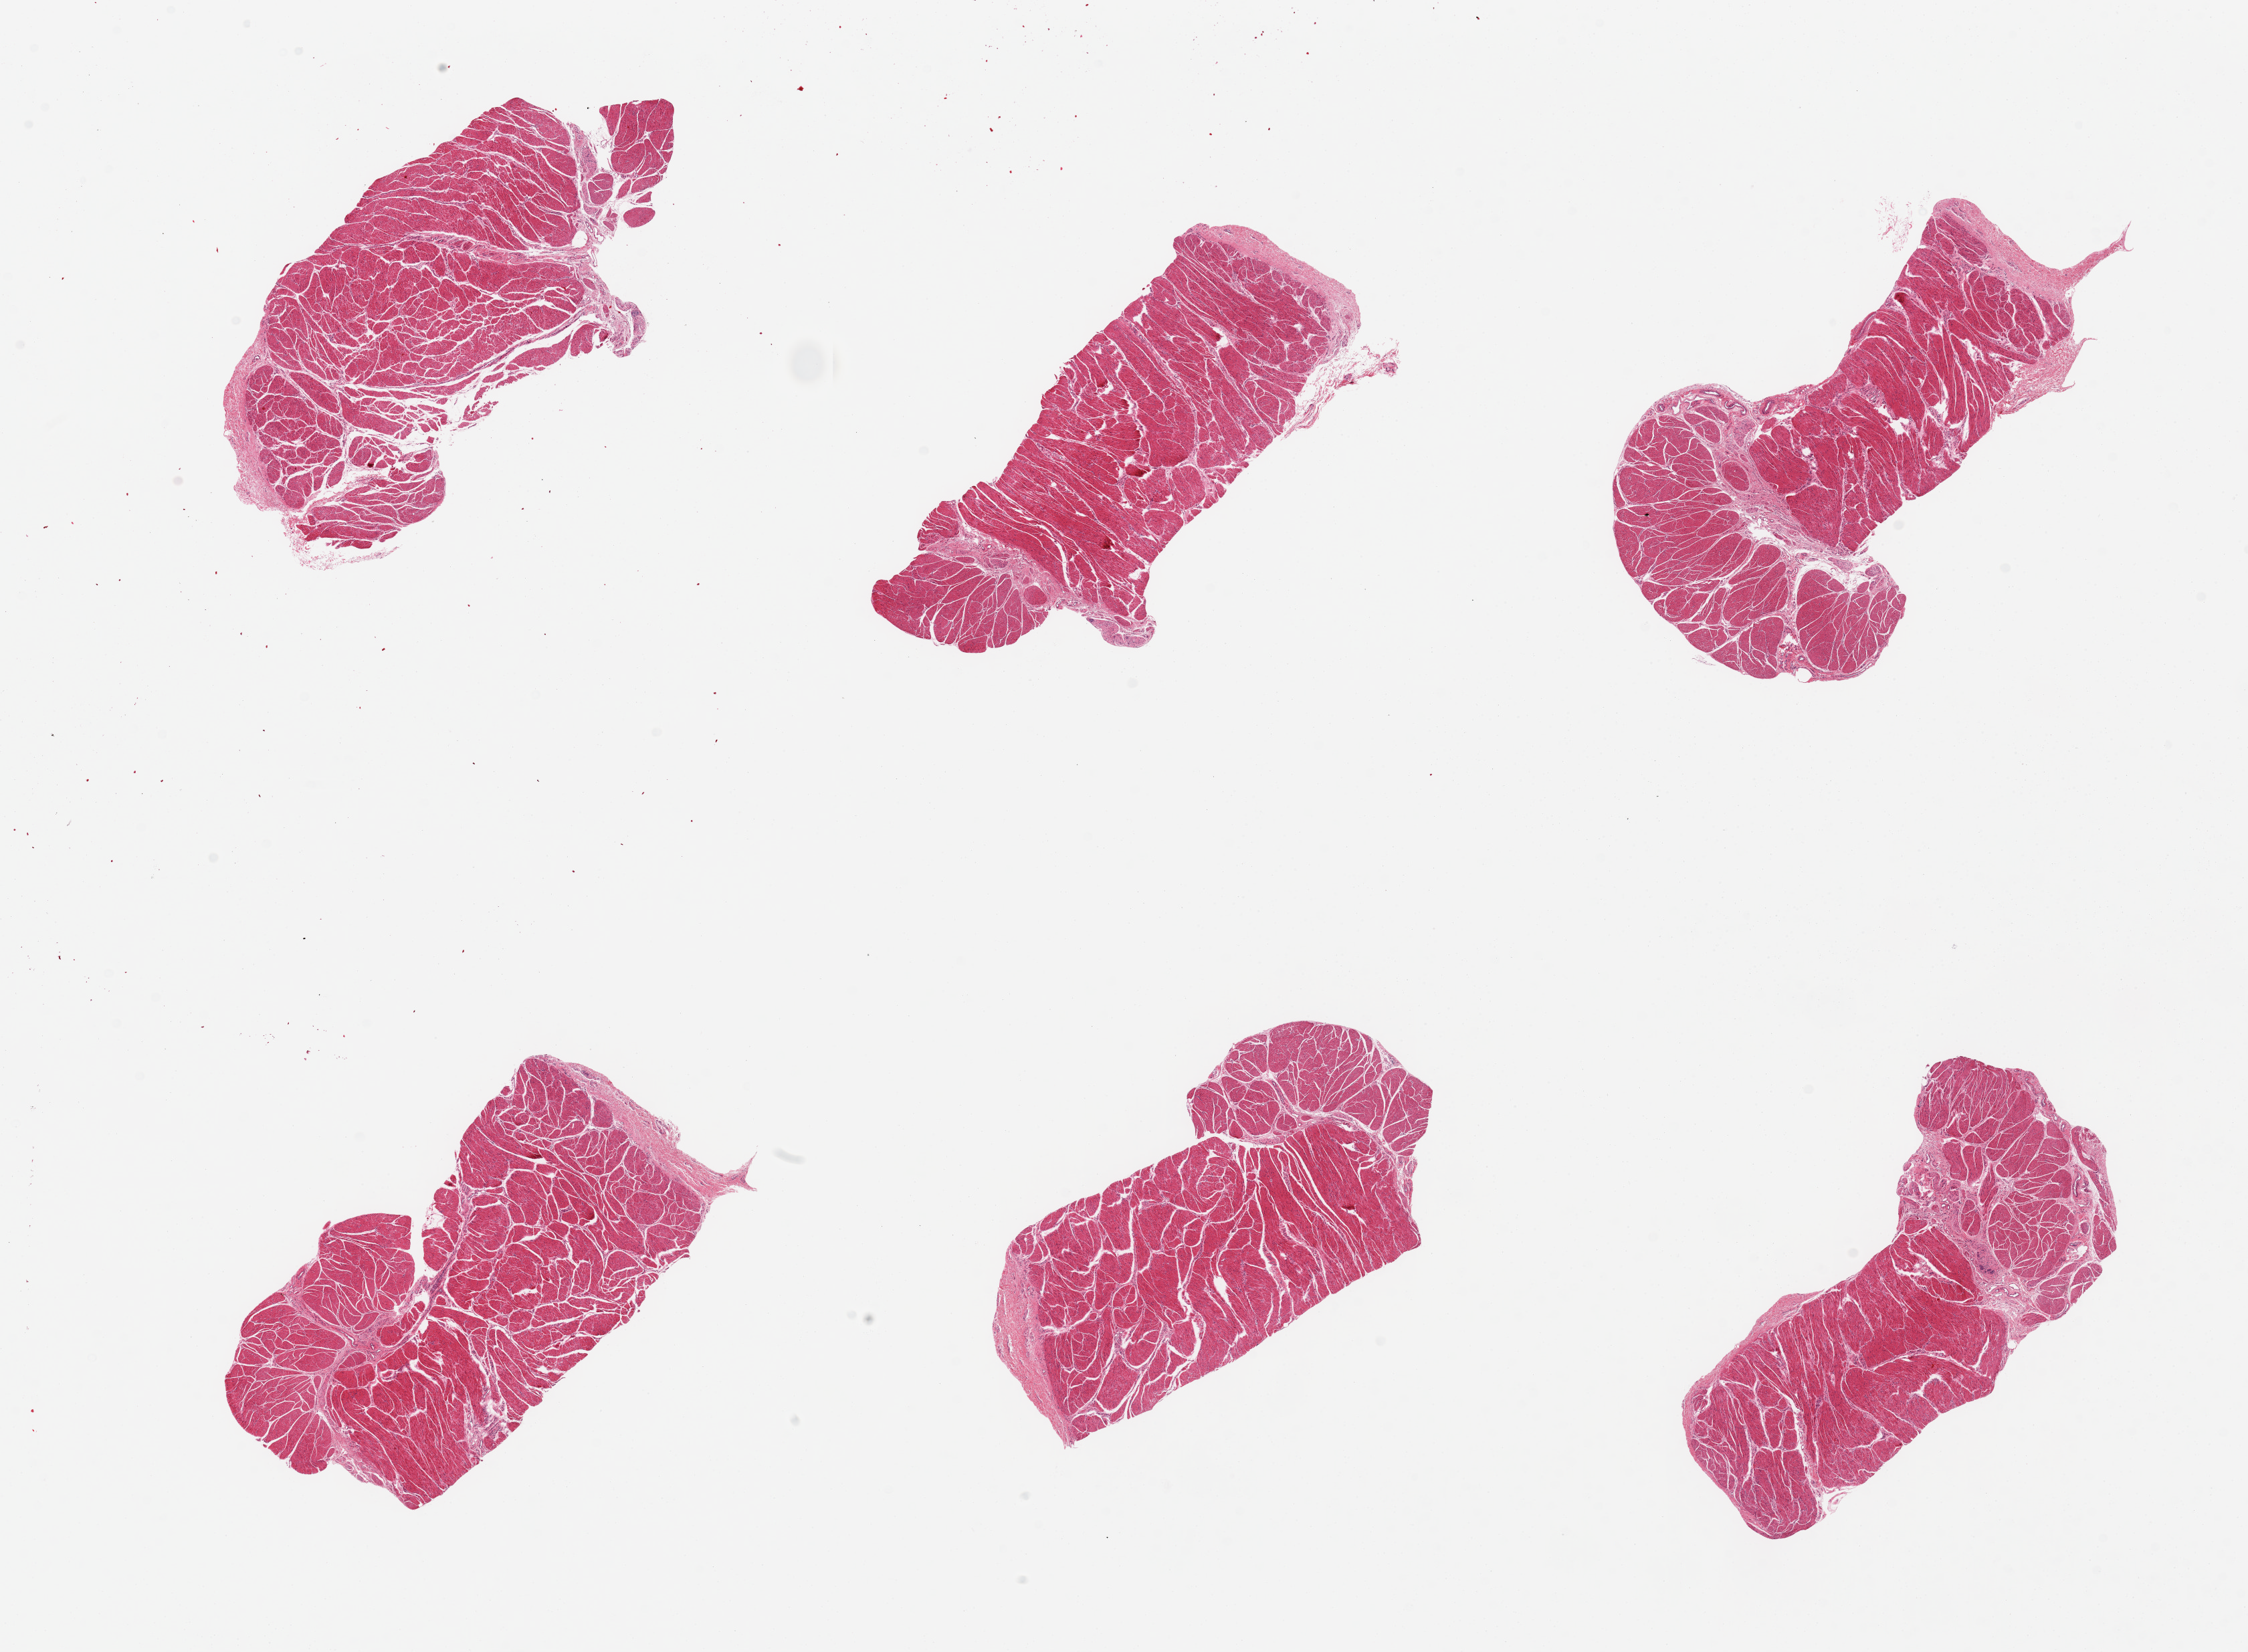
Digitized haematoxylin and eosin-stained section, low-resolution overview of the scanned area, about 26.6 x 19.5 mm, PAXgene-fixed, paraffin-embedded tissue, section of esophageal muscle (target tissue), tissue donor sample. Female donor.
Pathologist's review note for this sample: 6 pieces, well trimmed.